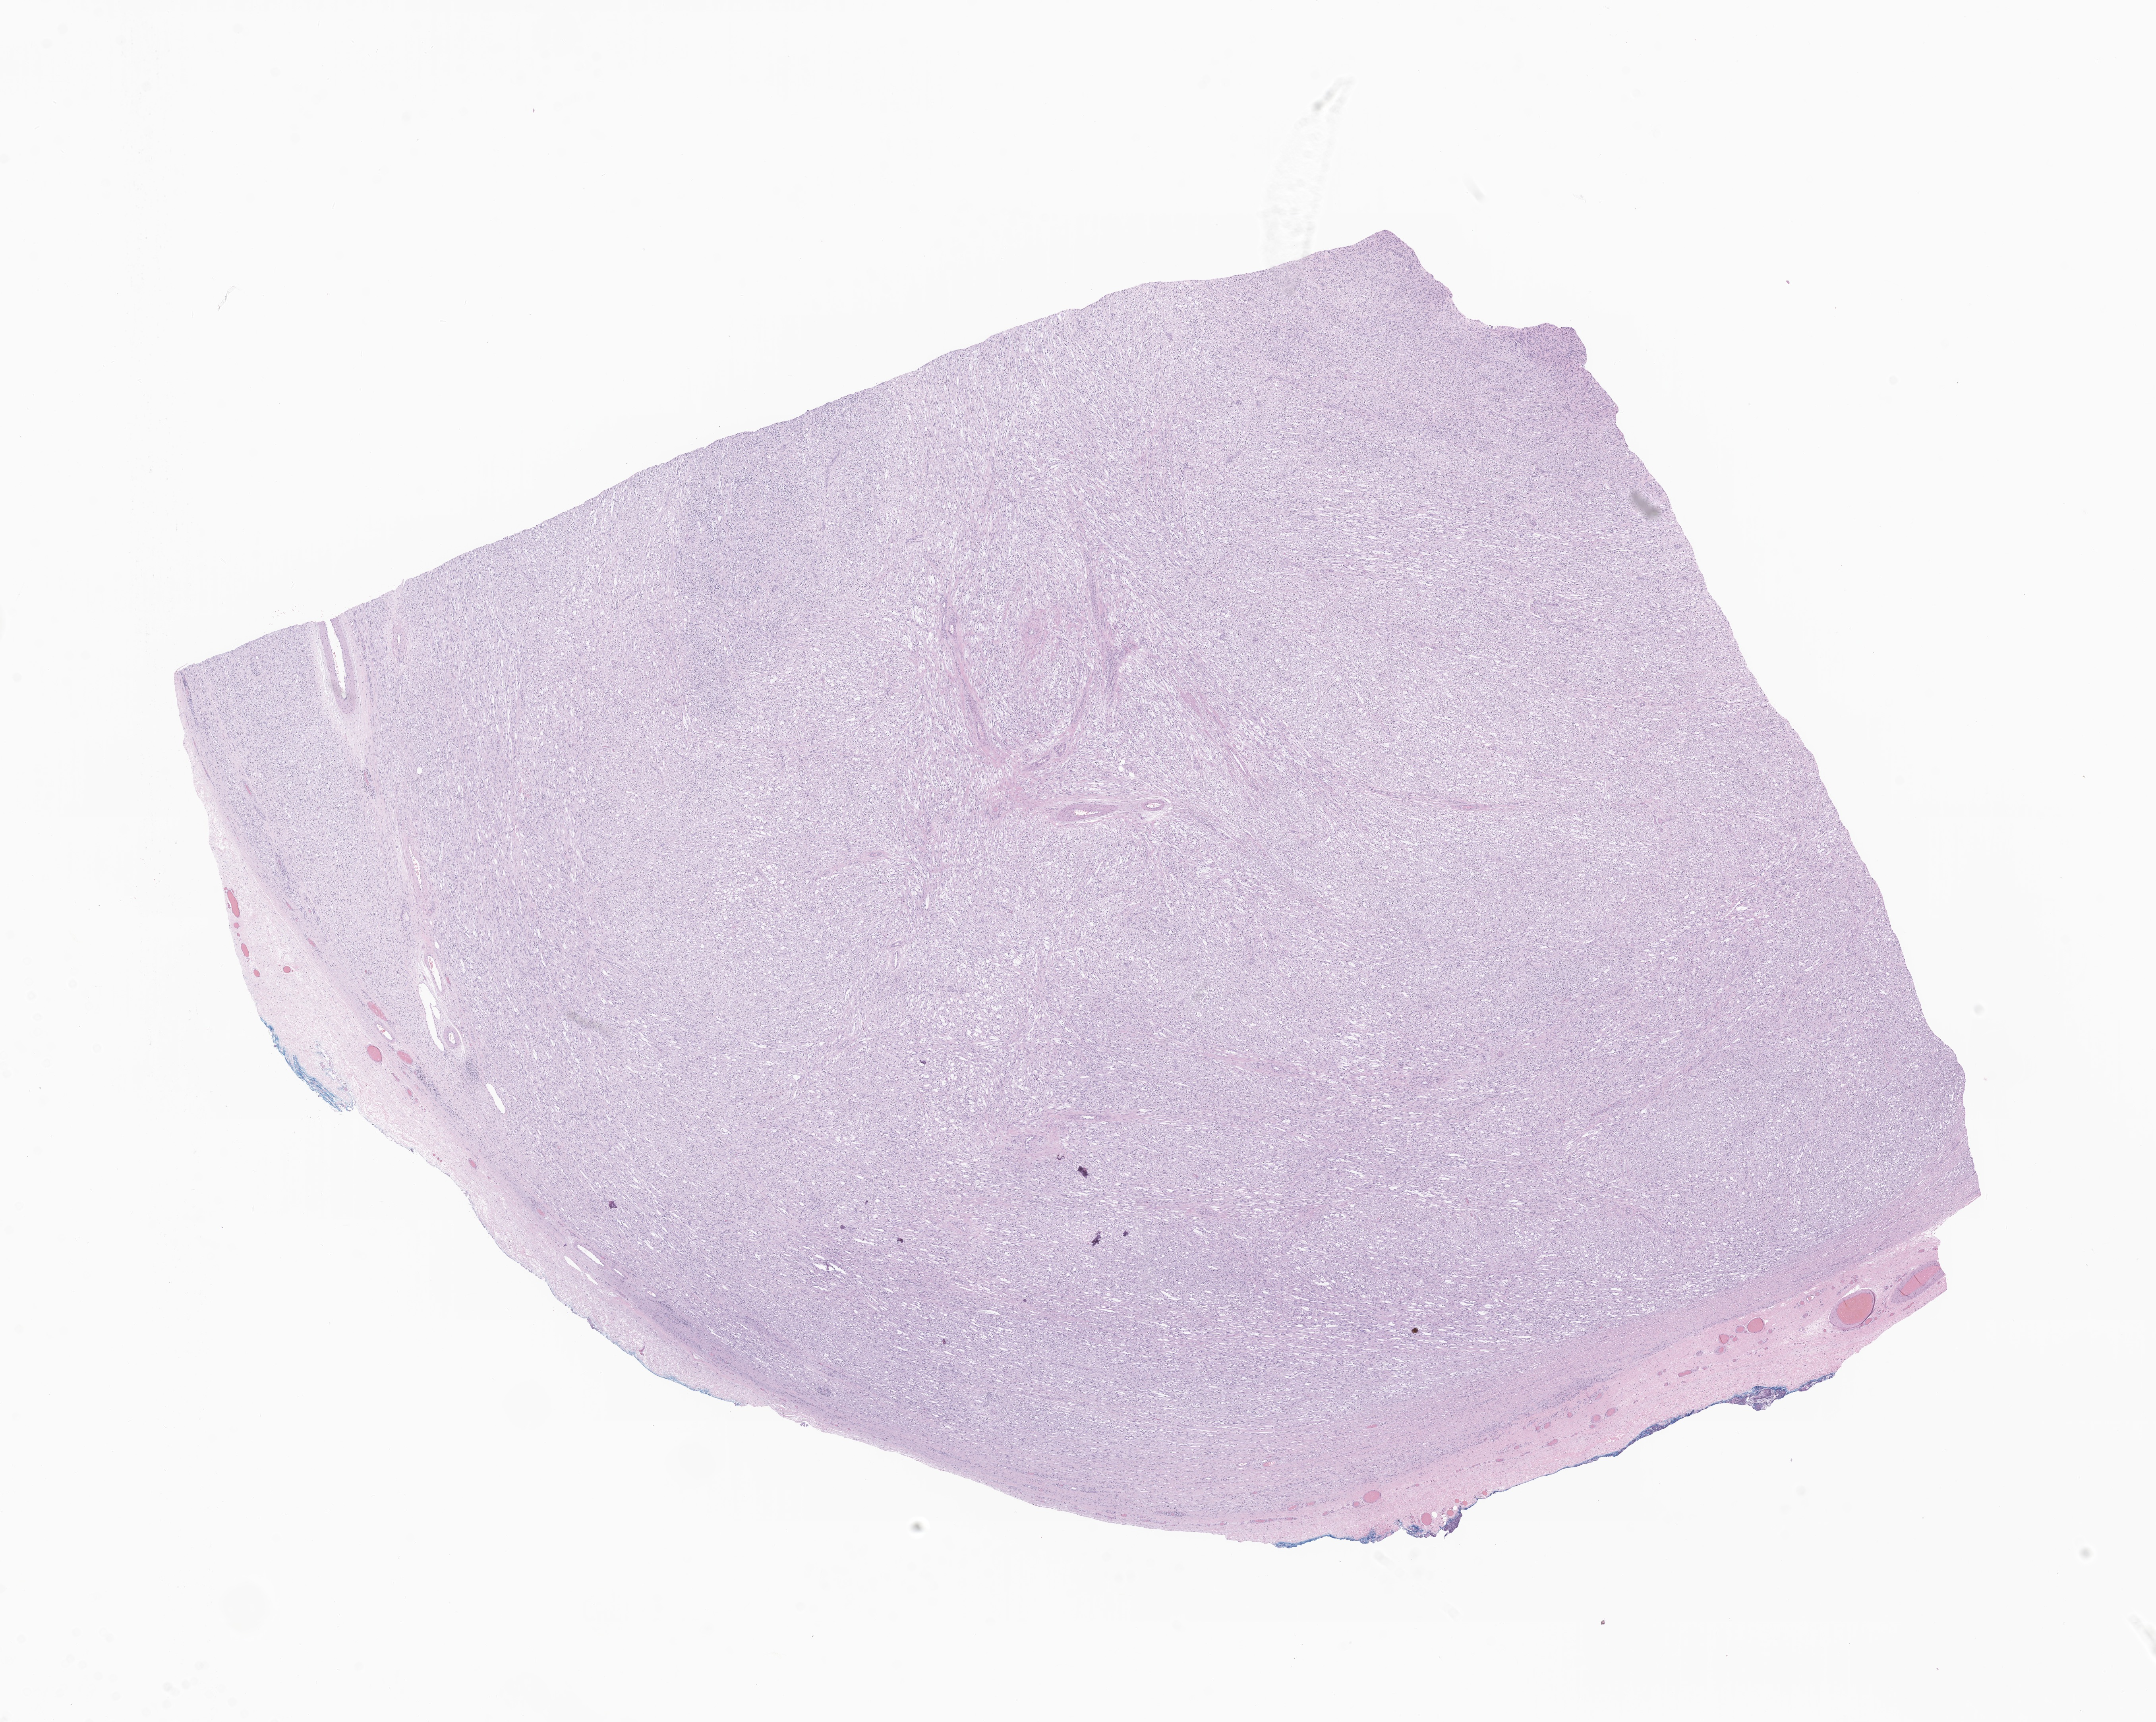
Whole-slide image, haematoxylin and eosin stain of tumor tissue from the testis — a low-resolution overview of the entire scanned area, about 22.9 x 18.3 mm; formalin-fixed, paraffin-embedded (FFPE) tissue. Male patient, age 182 months (15 years 2 months).
* recorded diagnosis: Spindle cell rhabdomyosarcoma